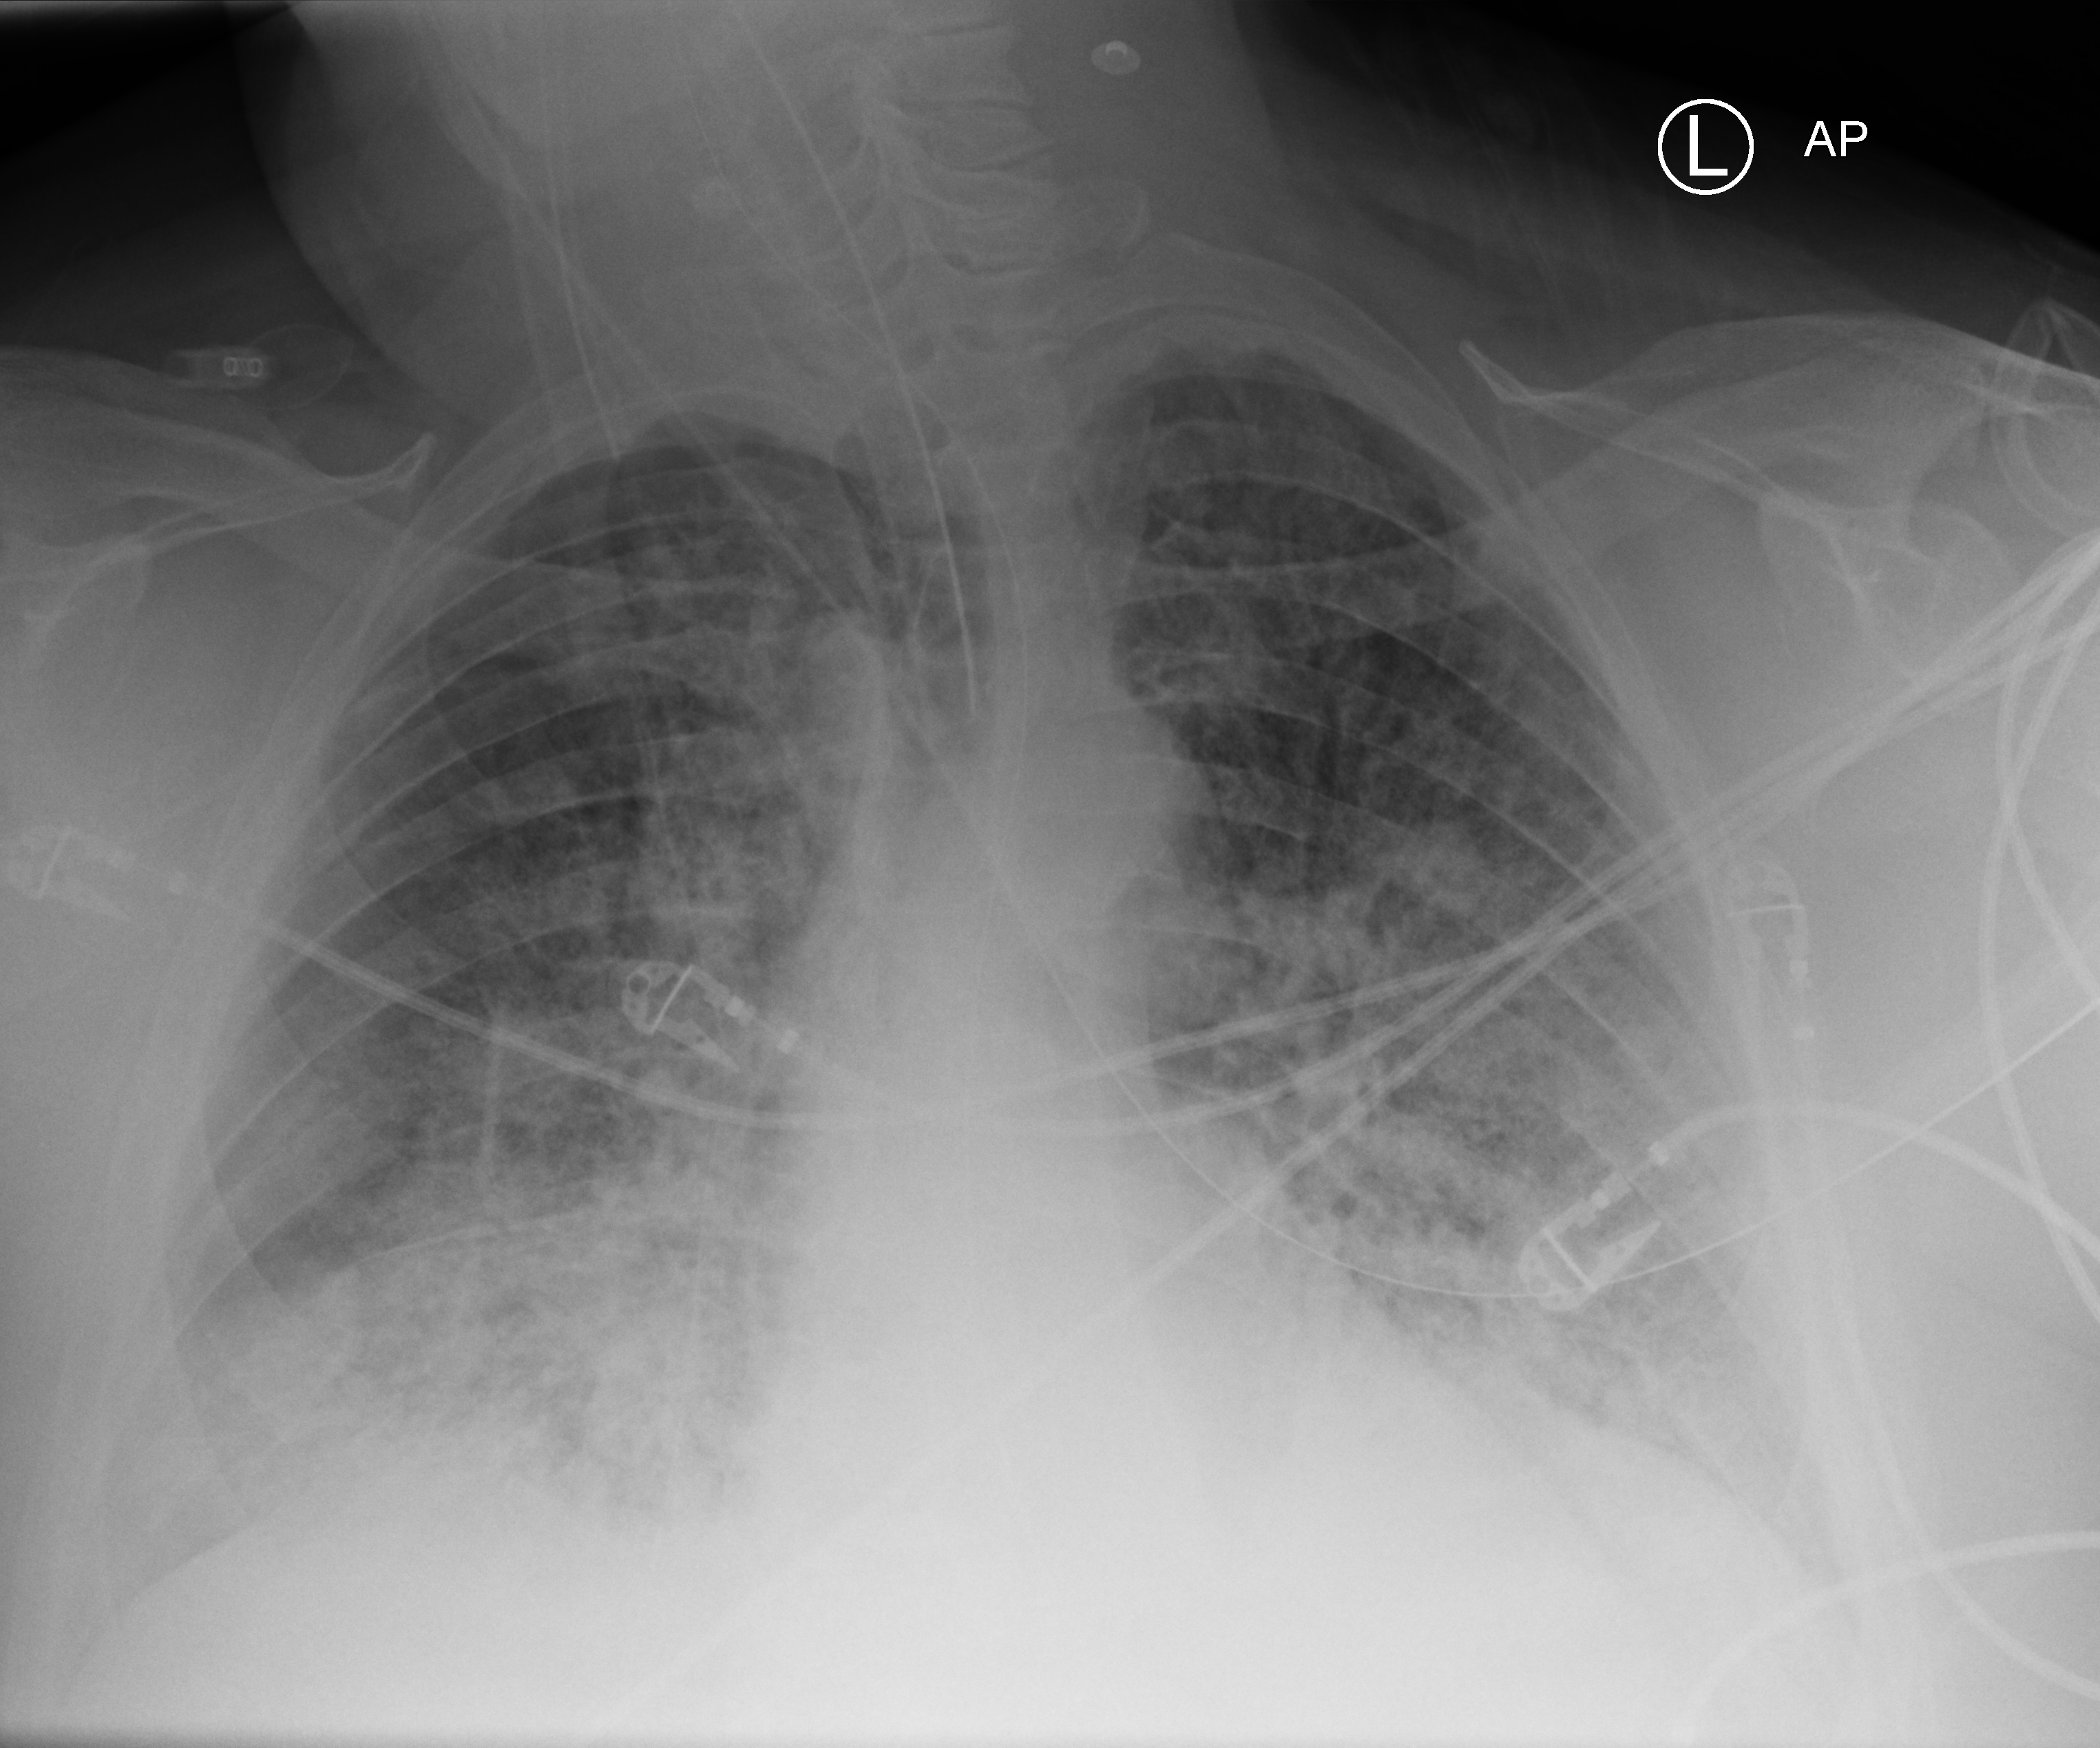
Portable chest radiograph, anteroposterior (AP) projection. Patient hospitalised with COVID-19; male, aged 60–74 years.
From the hospital-stay record, not from the radiograph (when in the stay this image was taken is not recorded): COPD (admission record): yes; admitted to intensive care during this hospital stay: yes.